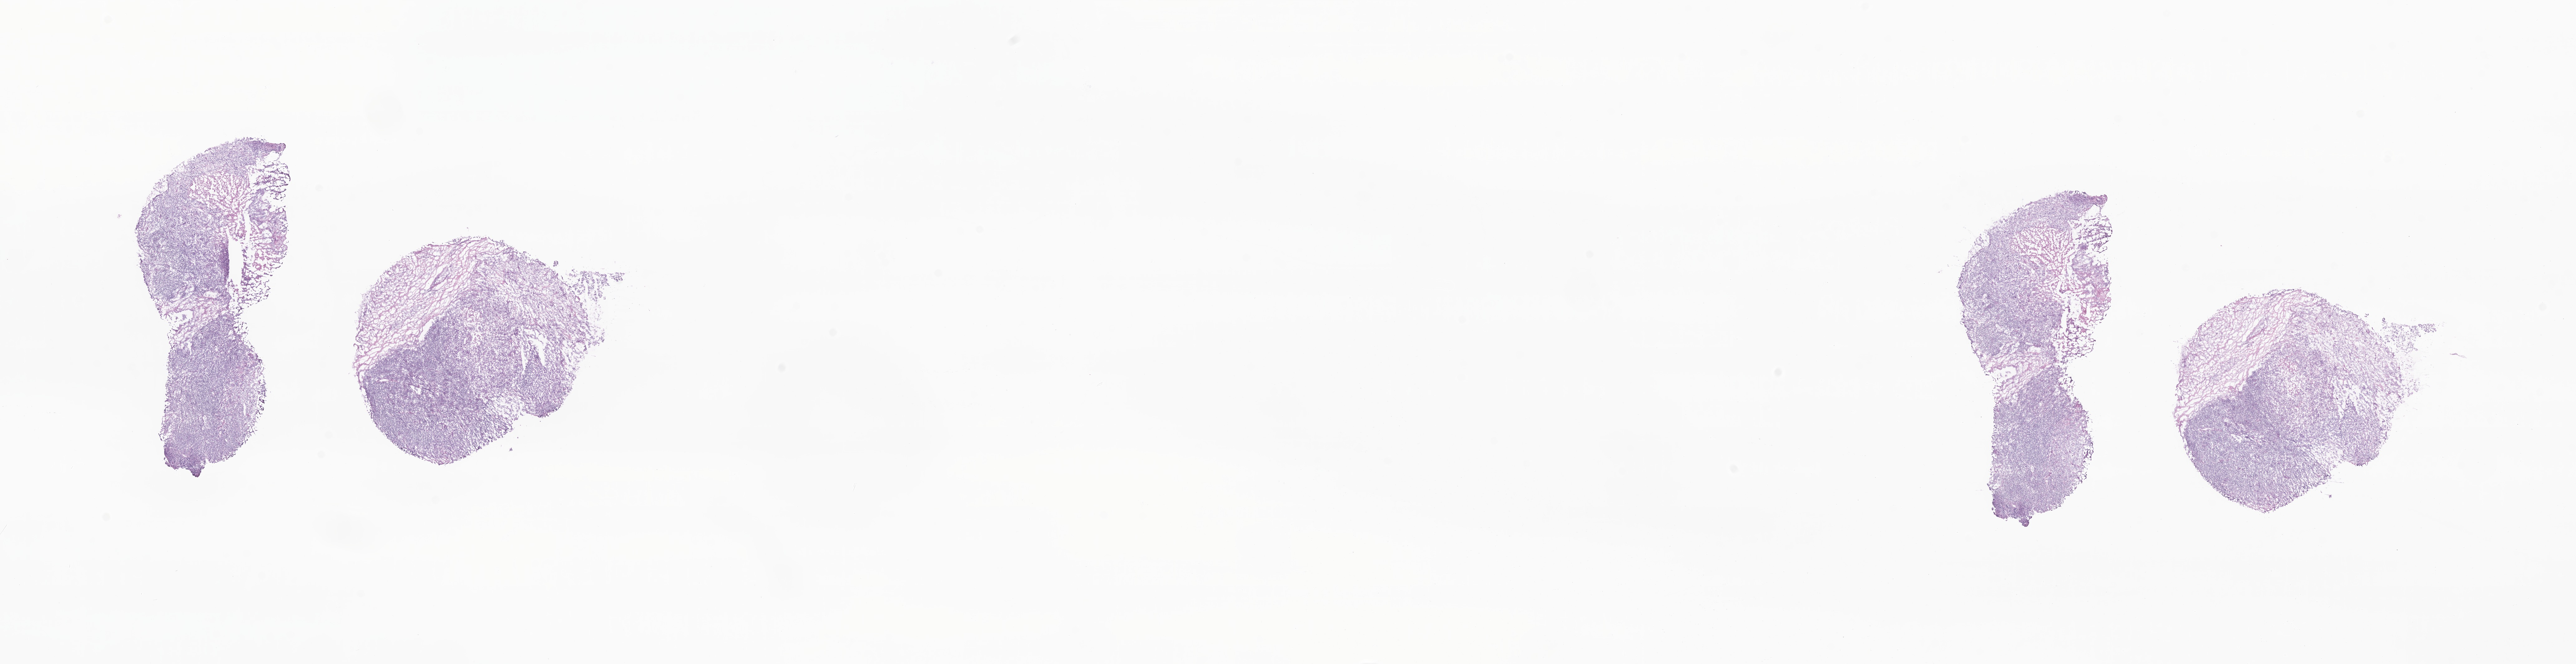
Digitized H&E-stained section, low-resolution overview of the scanned area, about 34.8 x 9.0 mm; frozen section (tissue freezing medium); specimen: metastatic tumor tissue, resected from lymph nodes of axilla or arm. Female patient; age at initial diagnosis 74 years. Slide review estimates, as recorded: tumor cells 75%, tumor nuclei 80%, stromal cells 0%, necrosis 10%, normal cells 15%. Inflammatory infiltration, as recorded: lymphocyte infiltration 0%, monocyte infiltration 0%, neutrophil infiltration 0%.
Patient diagnosis (primary): Infiltrating duct carcinoma, NOS. Section: top of the tissue portion.